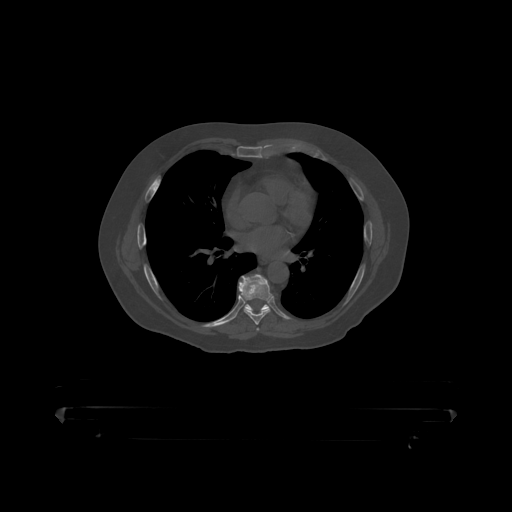
CT including the spine, one axial slice; position 272 of 390 along the scan axis; reconstruction kernel STANDARD; bone window (W 1800 / L 400 HU); 1.25 mm slice thickness; 512 × 512 image matrix, field of view 650 × 650 mm. Male patient, age 60 years. From the clinical record (not read from this slice): primary cancer: prostate.
Outlined on this slice (semi-automatically segmented with operator editing):
- T7 vertebra: bounding box [x1, y1, x2, y2] px = [239, 275, 273, 319]
- T8 vertebra: [245, 304, 270, 312]